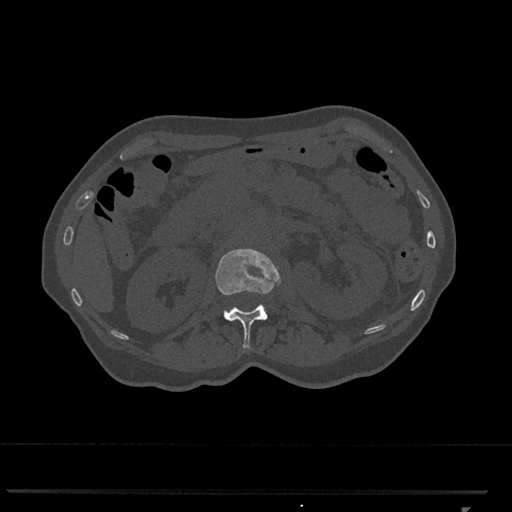
CT including the spine, one axial slice. Slice 392 of 793 in the series (ordered by position). 120 kVp. Bone window (W 1800 / L 400 HU). 512 × 512 image matrix, field of view 380 × 380 mm. Patient: female, 62 years. From the clinical record (not read from this slice): primary cancer: renal.
Annotated regions visible in this slice (semi-automatic segmentation, software-assisted and operator-edited):
- L1 vertebra: box from (x=215, y=248) to (x=281, y=349) px